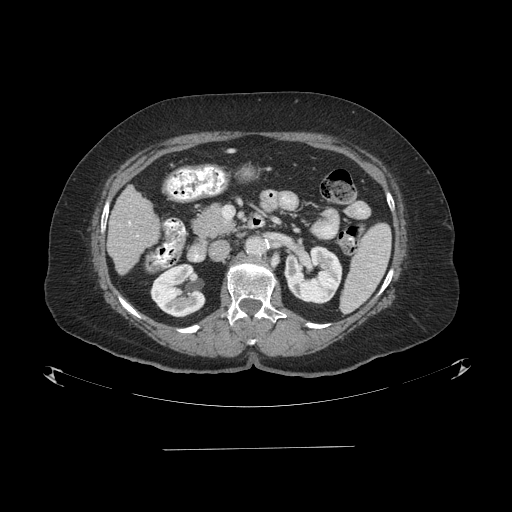
Contrast-enhanced abdominal CT (liver protocol), one axial slice. Slice 32 of 103 in the series (ordered by position). One of 2 acquisitions stored at this slice position. Soft-tissue window (W 400 / L 40 HU). 2.5 mm slice thickness. 512 × 512 image matrix, field of view 500 × 500 mm. Case-level facts recorded for this patient, not image findings: diagnosis: hepatocellular carcinoma (patient treated with transarterial chemoembolisation; whether this scan precedes or follows treatment is not stated here); TNM stage (as recorded): Stage-IIIA.
Outlined on this slice (semi-automatic segmentation, software-assisted and operator-edited):
- liver parenchyma outside the tumour (the mass and vessels are separate outlines, so this box may not span the whole liver): bounding box (x1, y1, x2, y2) in pixels: (106, 186, 159, 274)
- liver vessels: (129, 222, 131, 225)